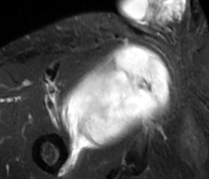
MRI of an extremity soft-tissue mass, one axial slice; slice 60 of 89 in the series (ordered by position); STIR; MR volume resampled by the dataset authors to the PET/CT grid (not the native acquisition matrix); 209 × 179 image matrix. Male patient. From the clinical record (not read from this slice): histological type: undifferentiated - pleiomorphic; grade: high; site of the primary tumour: right thigh.
Structures marked on this image (expert contour drawn on MRI and transferred to this co-registered scan by the dataset authors):
- gross tumour volume including surrounding oedema: bounding box (x1, y1, x2, y2) in pixels: (62, 44, 170, 149)
- gross tumour volume (mass): (62, 44, 170, 149)